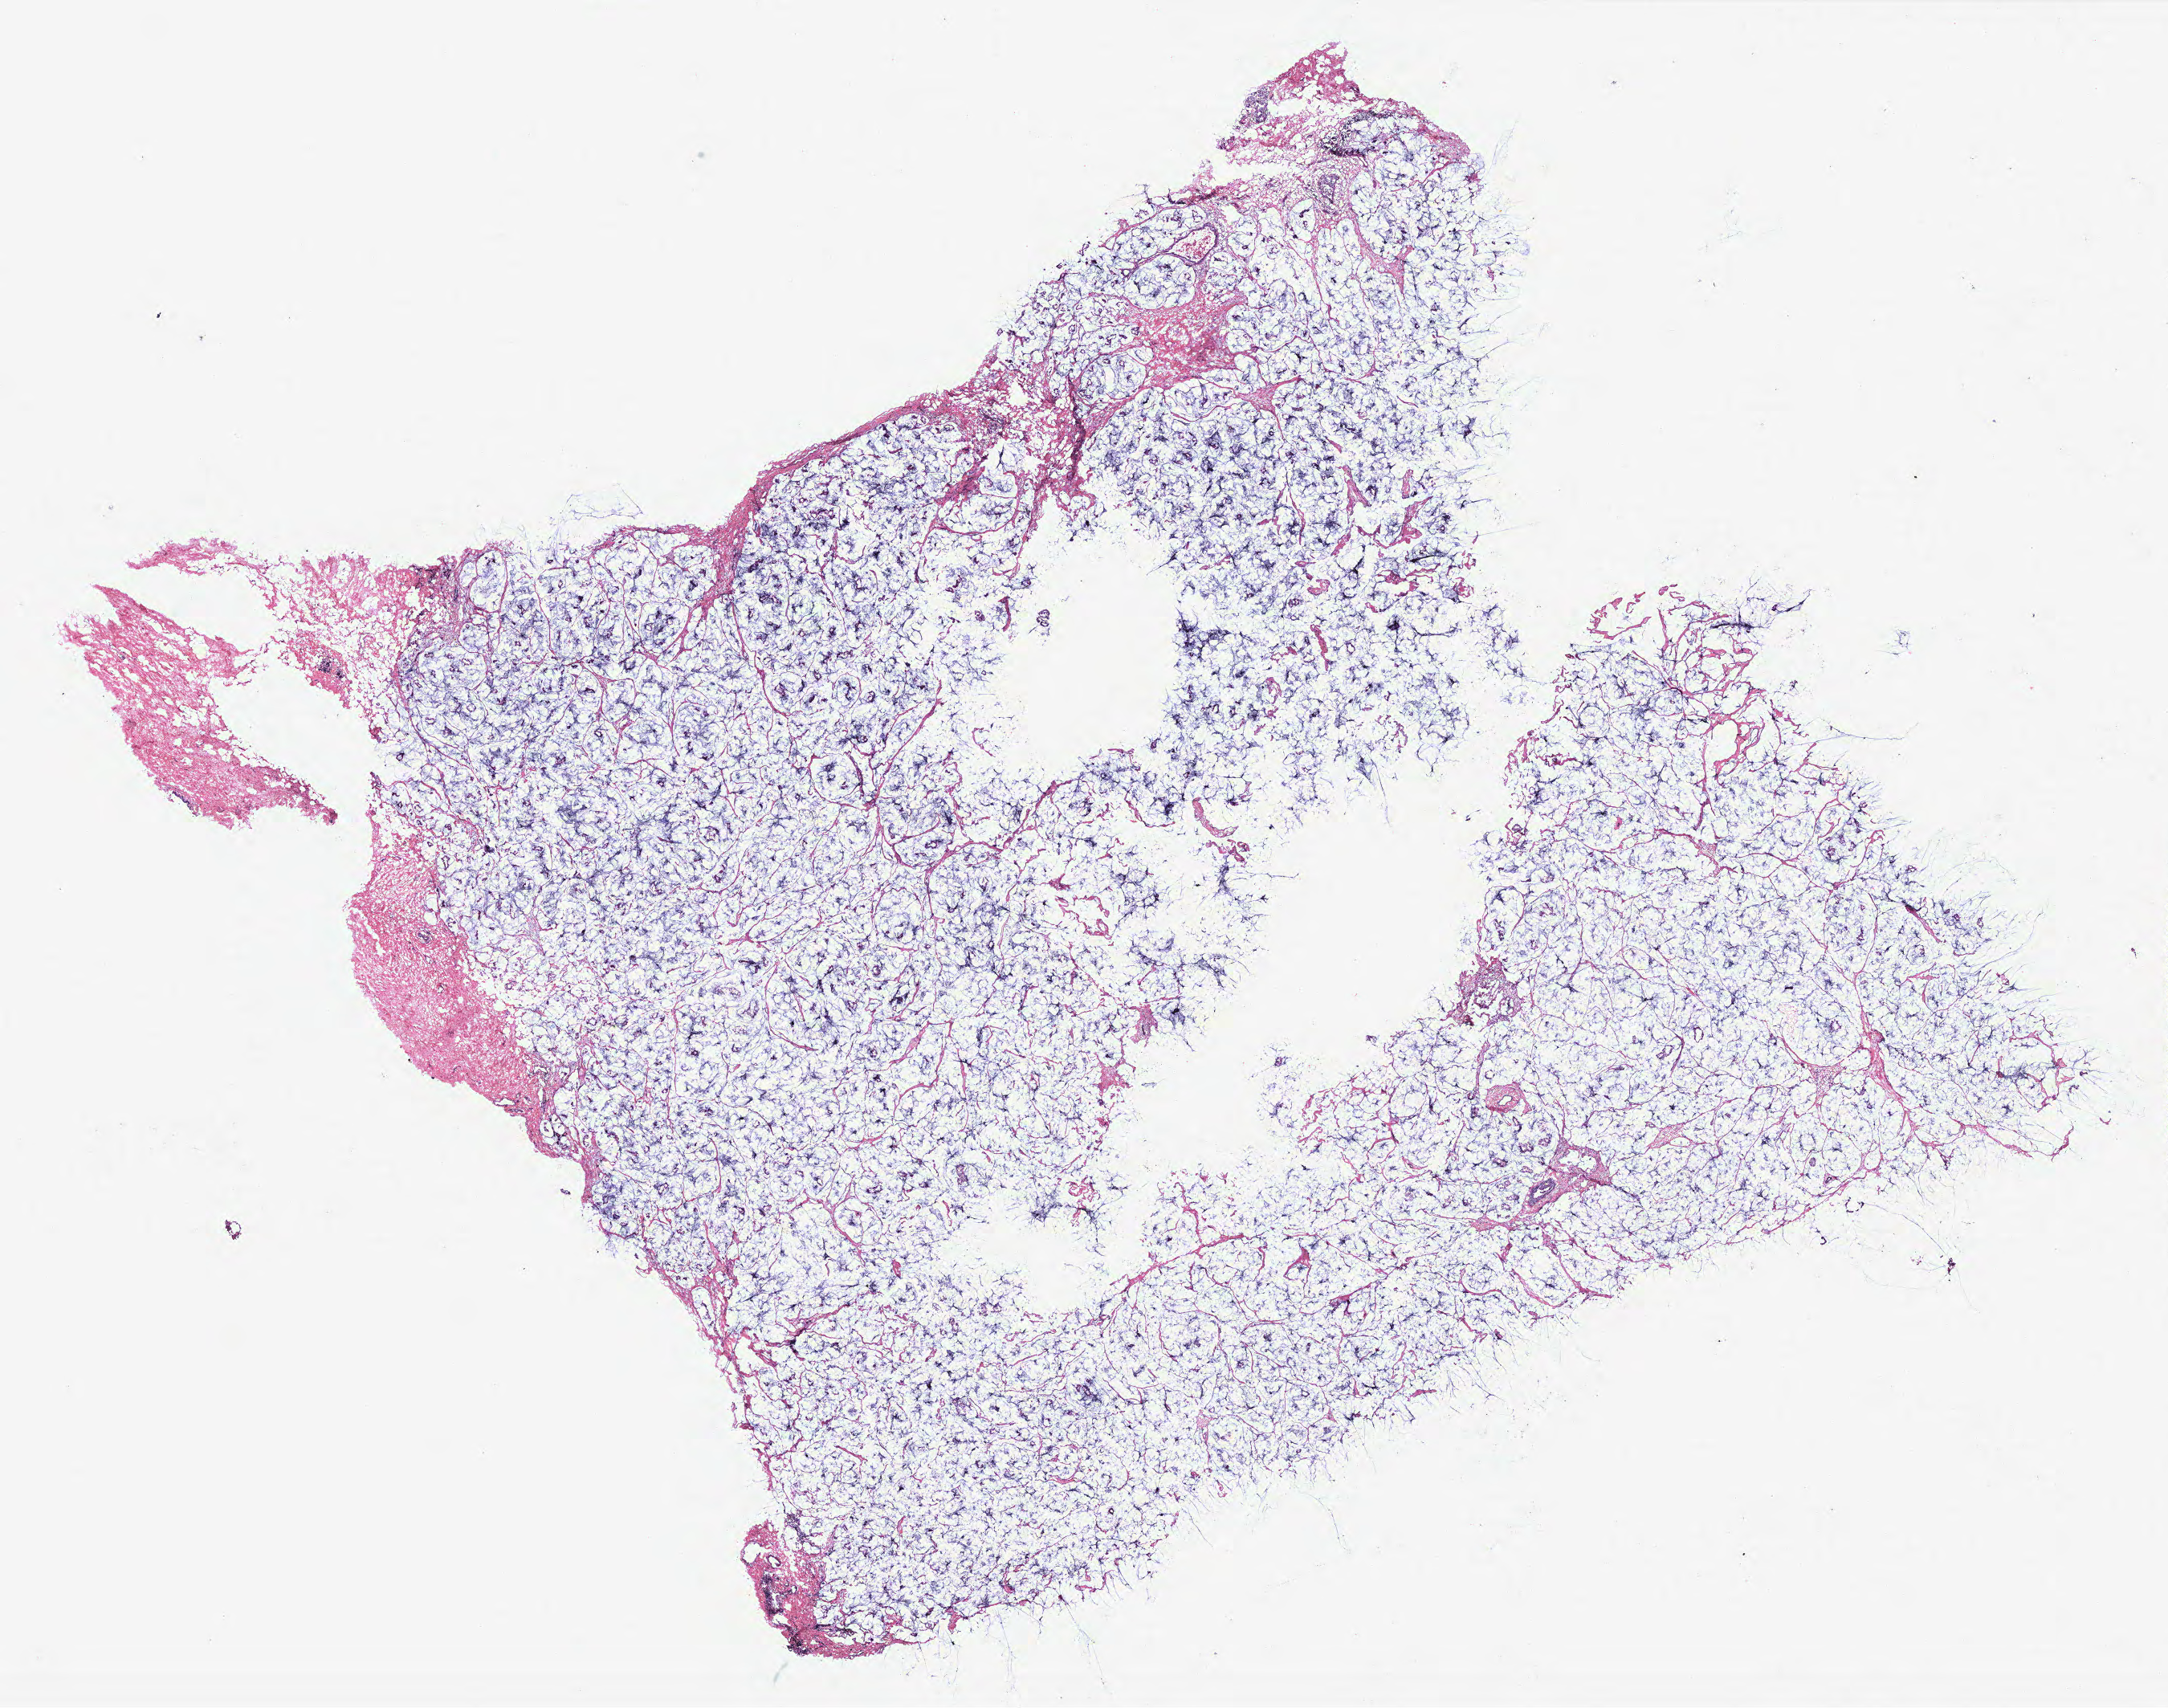
Digitized H&E tissue section (whole slide), a low-resolution overview of the entire scanned area, about 21.6 x 17.0 mm; breast, tissue type not recorded. 53-year-old female patient.
Patient diagnosis: Mucinous carcinoma.